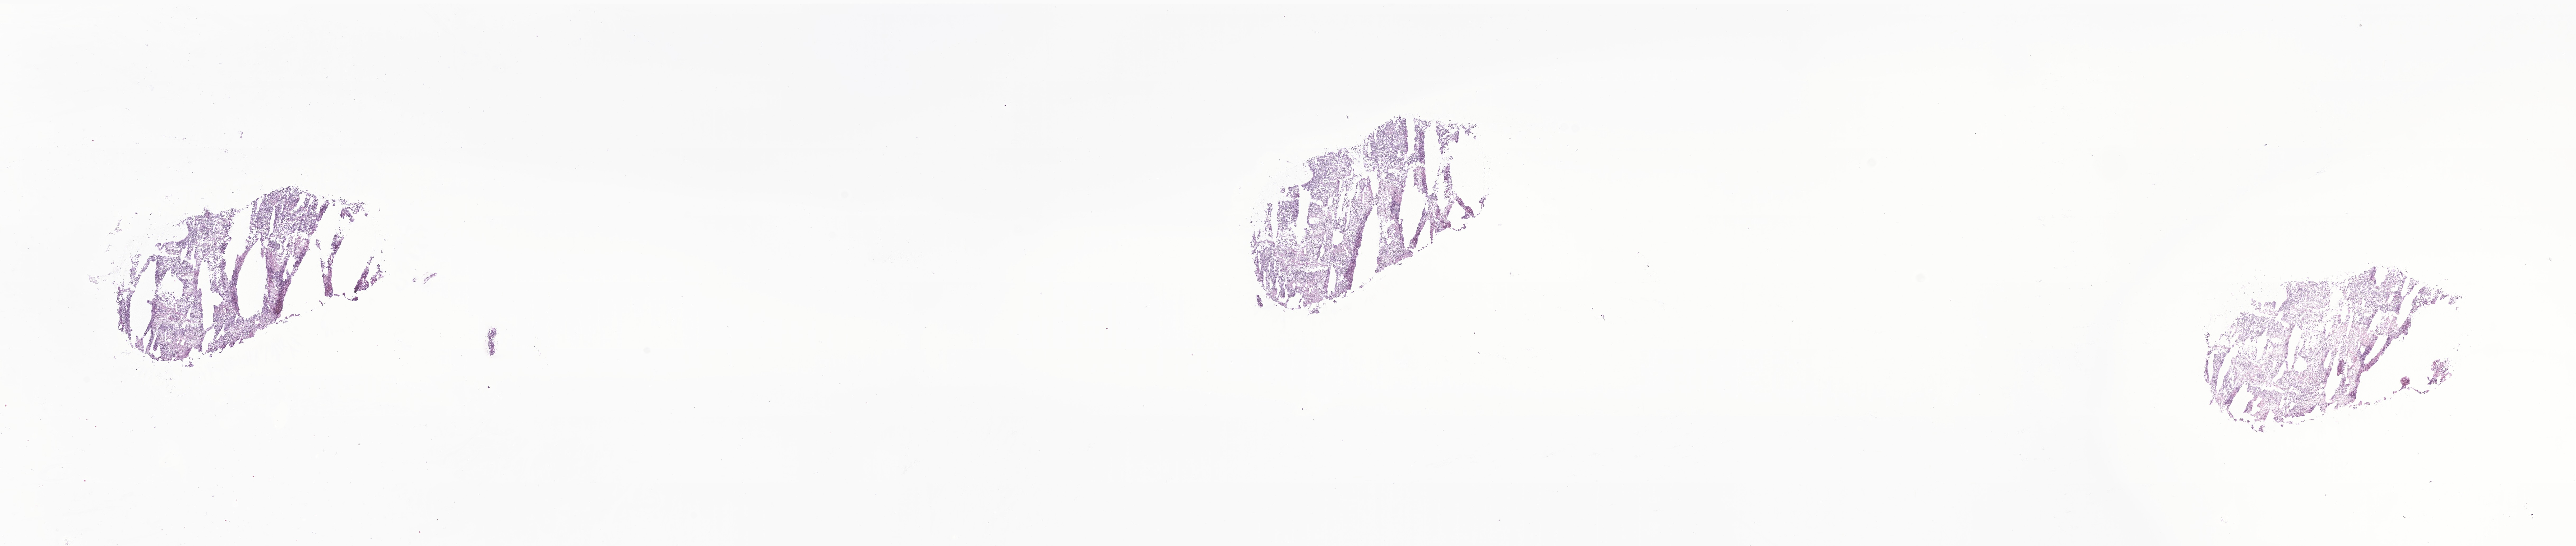
Digitized haematoxylin and eosin-stained section of tumor tissue from the adrenal gland, whole scanned area (about 41.1 x 8.7 mm) shown as a low-resolution overview. Frozen section. Female patient, age 155 days.
- diagnosis (ICD-O-3 morphology term): Neuroblastoma, NOS